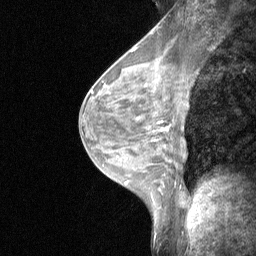
Breast MRI (dynamic contrast-enhanced), one sagittal slice; slice 33 of 64 in the series (ordered by position); dynamic contrast-enhanced study with each time point stored as its own series, time point 2 of 3 at this slice position (early post-contrast, ordered by acquisition time); 1.5 T; TE 4.8 ms, TR 27 ms; 256 × 256 image matrix, field of view 200 × 200 mm. Patient: female, 44 years. Case-level facts recorded for this patient, not image findings: setting: breast cancer imaged before/during neoadjuvant chemotherapy; receptor status: HR-positive, HER2-negative.
Outlined on this slice (semi-automatic segmentation, software-assisted and operator-edited):
- analysis volume of interest (the breast-tissue region the enhancement analysis was run in; not a lesion): bounding box (x1, y1, x2, y2) in pixels: (140, 109, 180, 148)
- tumour enhancement mask (voxels above the 90 % enhancement threshold inside the analysis volume of interest): (161, 129, 164, 131)